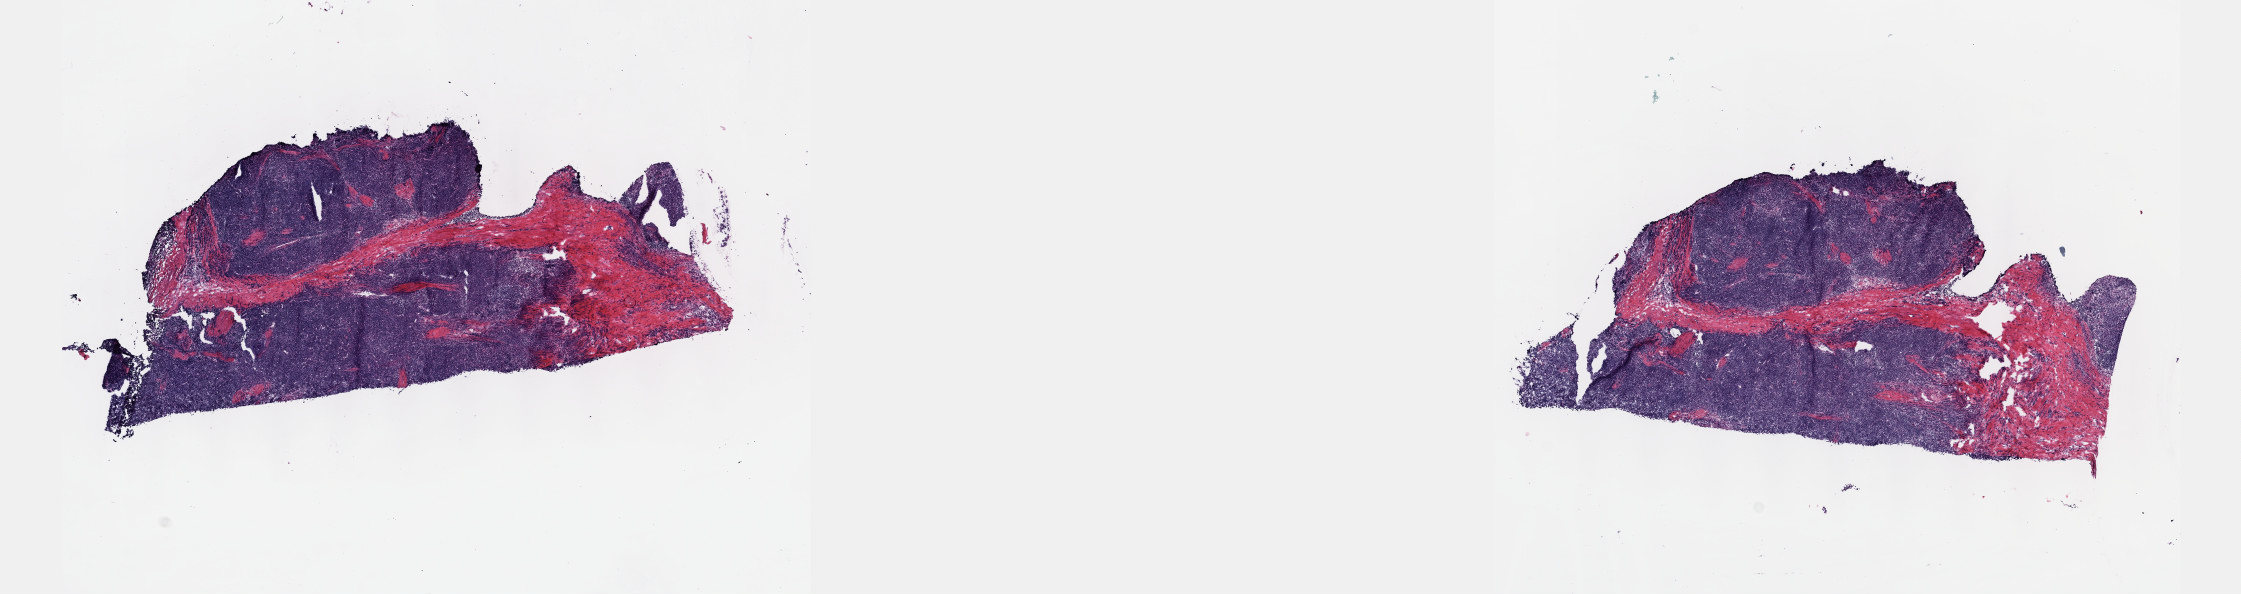
H&E-stained whole-slide image, low-resolution overview of the scanned area, about 18.1 x 4.8 mm (from a 40x scan). Frozen section. Primary tumour sample from the thymus. Female patient; age at initial diagnosis 48 years. Slide review estimates, as recorded: tumour cells 80%, tumour nuclei 90%, normal cells 0%, stromal cells 20%, necrosis 0%. Inflammatory infiltration, as recorded: lymphocyte infiltration 0%, monocyte infiltration 0%, neutrophil infiltration 0%.
Histologic diagnosis: Thymoma, type B2, malignant.